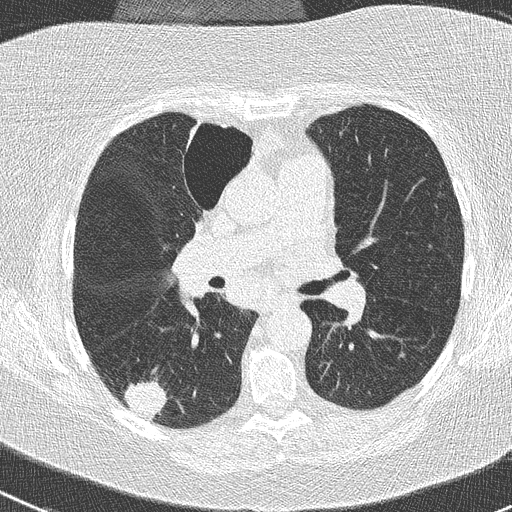
Low-dose screening chest CT, one axial slice; position 149 of 261 along the scan axis; 120 kVp; lung window (W 1500 / L -600 HU); 2 mm slice thickness; 512 × 512 image matrix, field of view 310 × 310 mm.
Outlined on this slice (manually delineated by an expert):
- lesion 1 (tumor, lower lobe of right lung): bounding box [x1, y1, x2, y2] px = [124, 381, 167, 420]